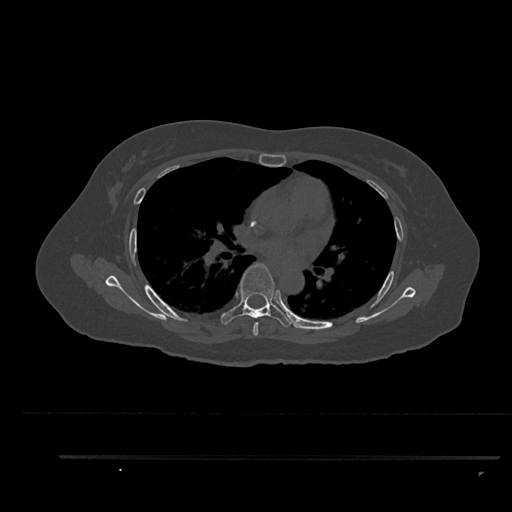
CT including the spine, one axial slice; position 567 of 797 along the scan axis; reconstruction kernel Br40s/3; 120 kVp; bone window (W 1800 / L 400 HU); 0.5 mm slice thickness; 512 × 512 image matrix, field of view 408 × 408 mm. Female patient, age 44 years. From the clinical record (not read from this slice): primary cancer: renal; vertebrae with lytic lesions (as recorded): L1.
Outlined on this slice (semi-automatically segmented with operator editing):
- T5 vertebra: box from (x=253, y=322) to (x=258, y=336) px
- T6 vertebra: (x=221, y=263)–(x=295, y=328)